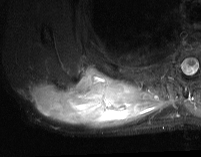
MRI of an extremity soft-tissue mass, one axial slice. Position 24 of 74 along the scan axis. STIR. MR volume resampled by the dataset authors to the PET/CT grid (not the native acquisition matrix). 3.27 mm slice thickness. 201 × 157 image matrix. Male patient. Case-level facts recorded for this patient, not image findings: histological type: pleiomorphic spindle cell undifferentiated; grade: high; site of the primary tumour: right parascapusular.
Structures marked on this image (expert contour drawn on MRI and transferred to this co-registered scan by the dataset authors):
- gross tumour volume including surrounding oedema: bounding box <28,66,166,129> (left, top, right, bottom; pixels)
- gross tumour volume (mass): <33,68,146,126>